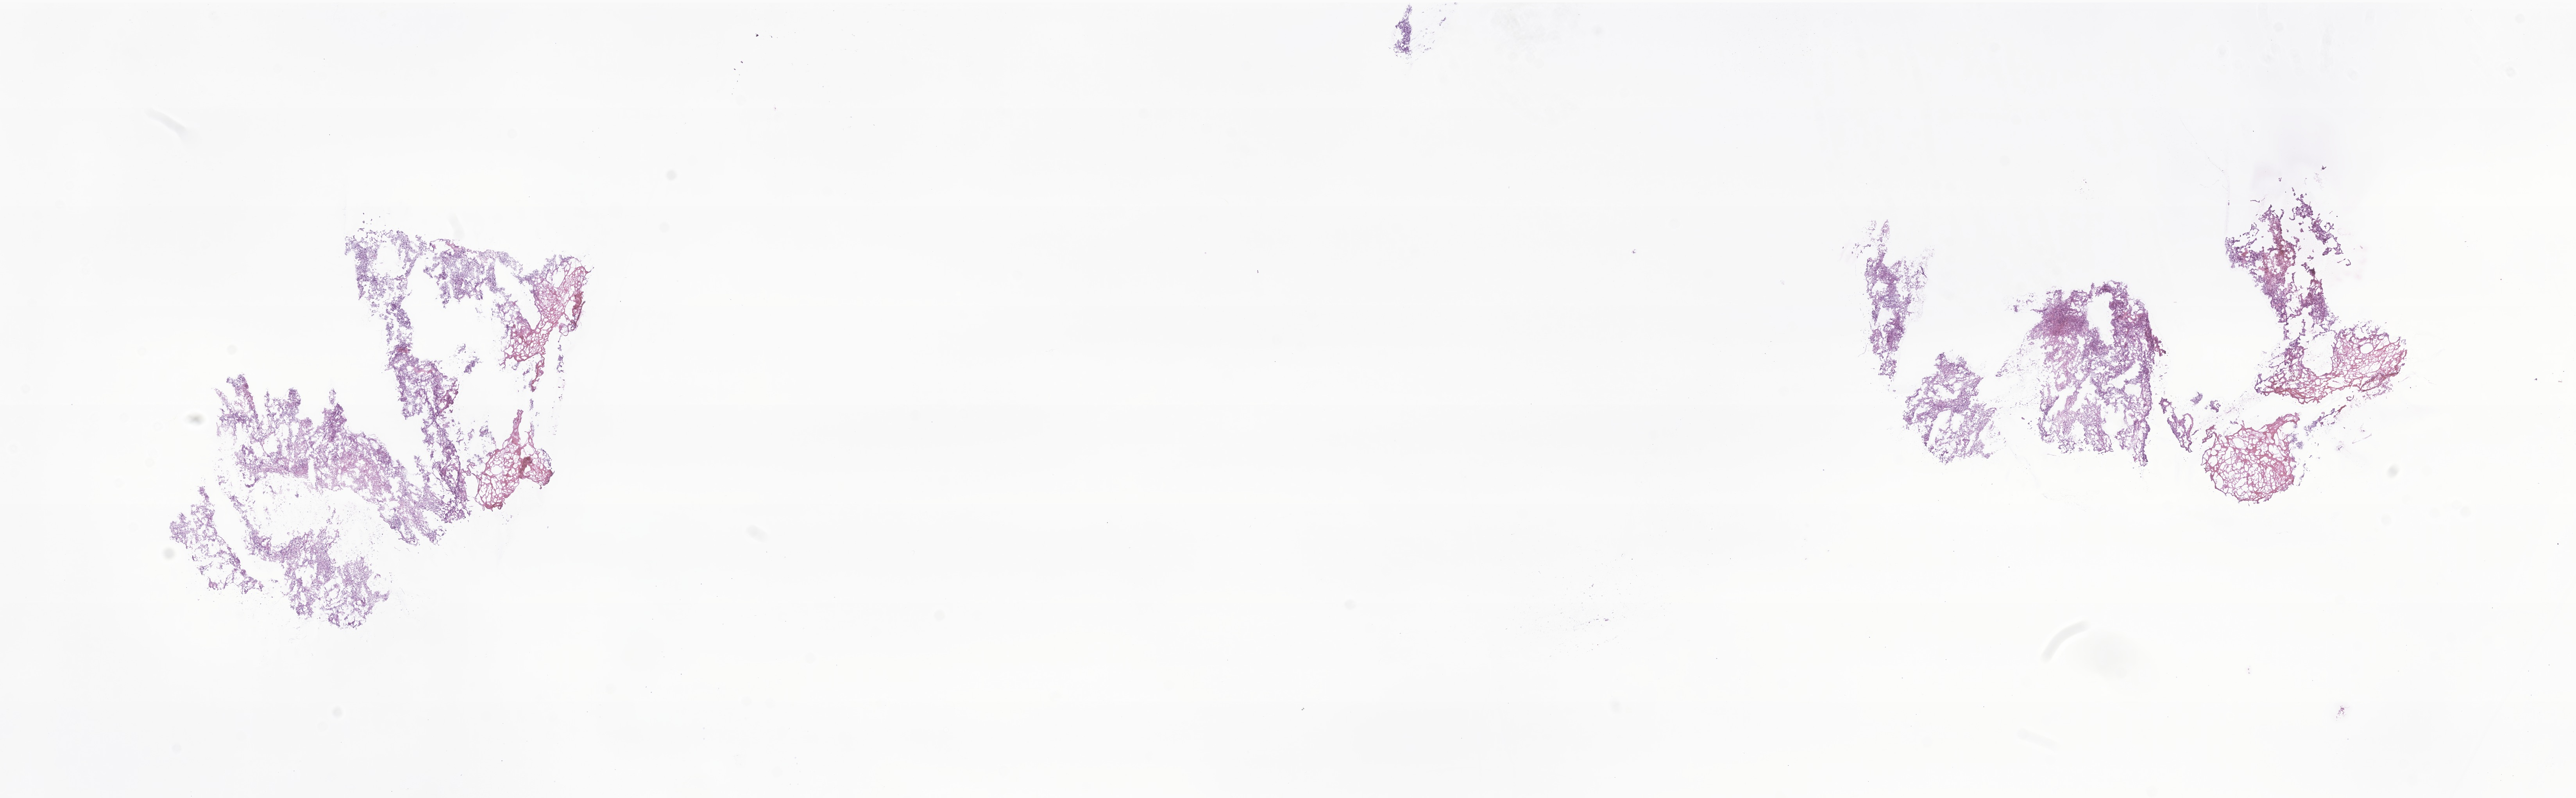
Hematoxylin and eosin (H&E) whole-slide image of tumor tissue from the brain, whole scanned area (about 27.8 x 8.6 mm) shown as a low-resolution overview; frozen section. Male patient, age 141 months (11 years 9 months).
Recorded diagnosis: Pilocytic astrocytoma.